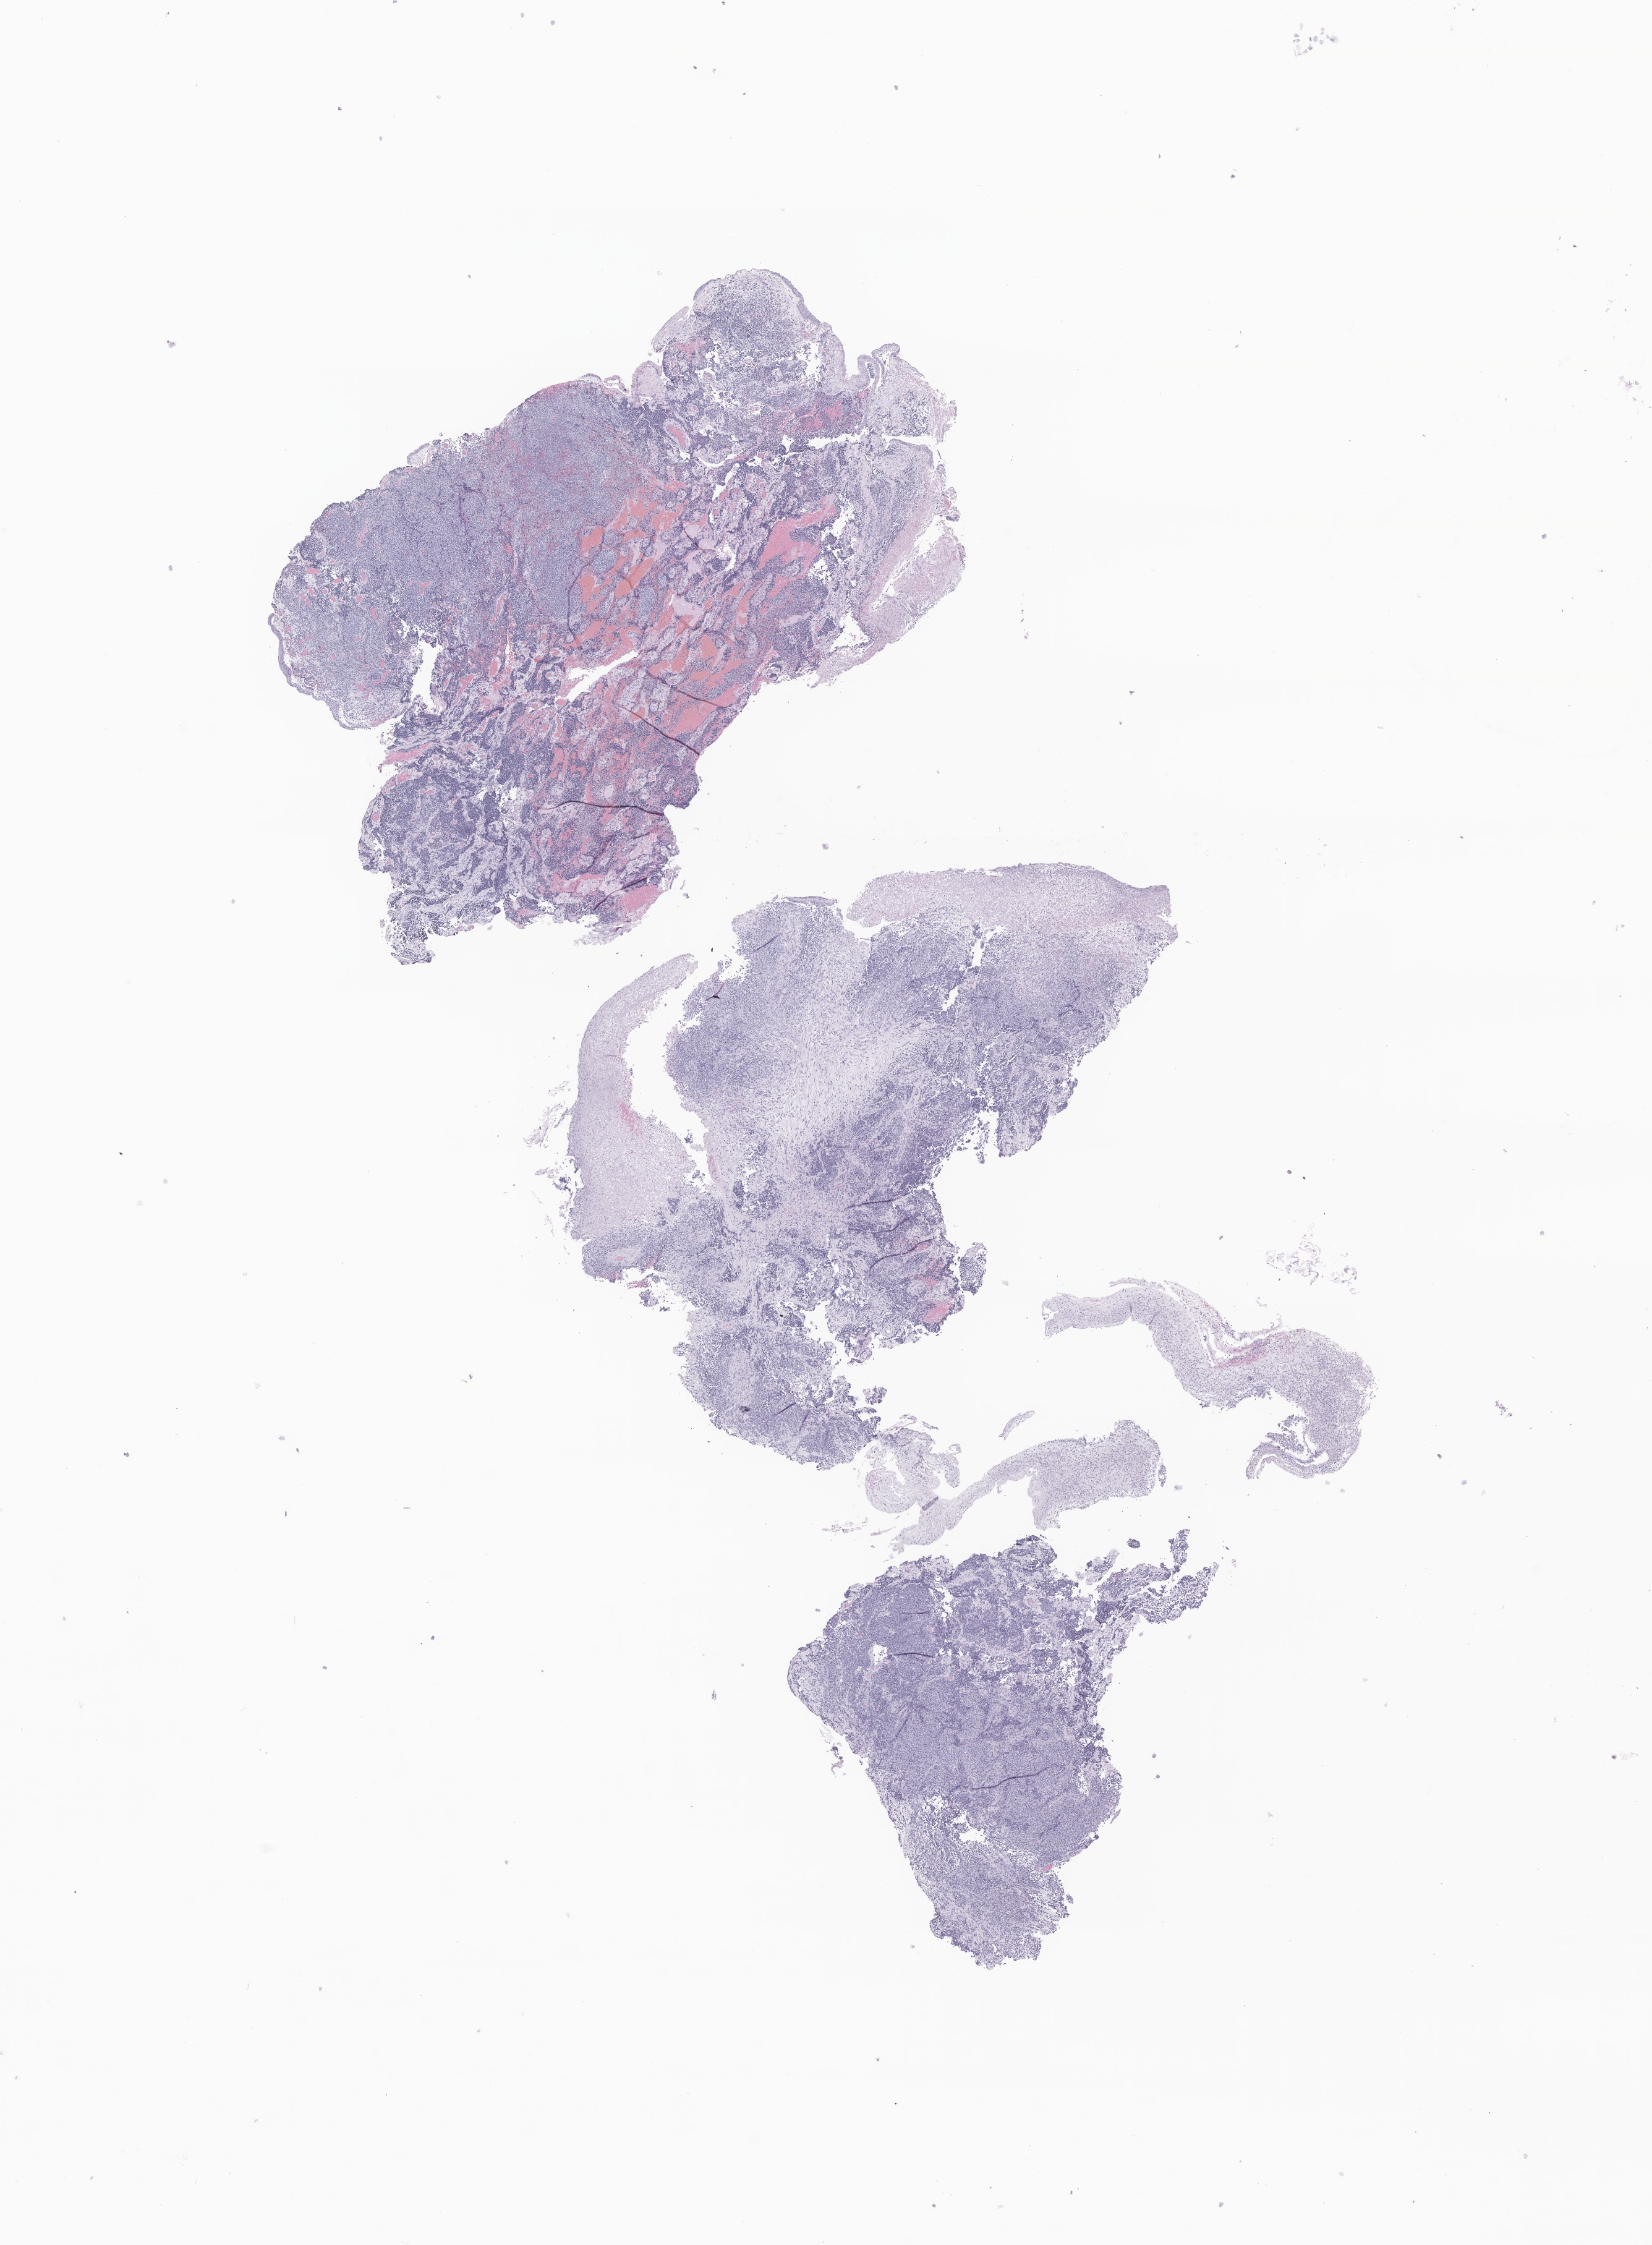
Hematoxylin and eosin (H&E) whole-slide image of tumor tissue from the nasal cavity — whole scanned area (about 11.3 x 15.3 mm) shown as a low-resolution overview, formalin-fixed, paraffin-embedded (FFPE) tissue. Patient: male, age 283 days.
Recorded diagnosis: Alveolar rhabdomyosarcoma.